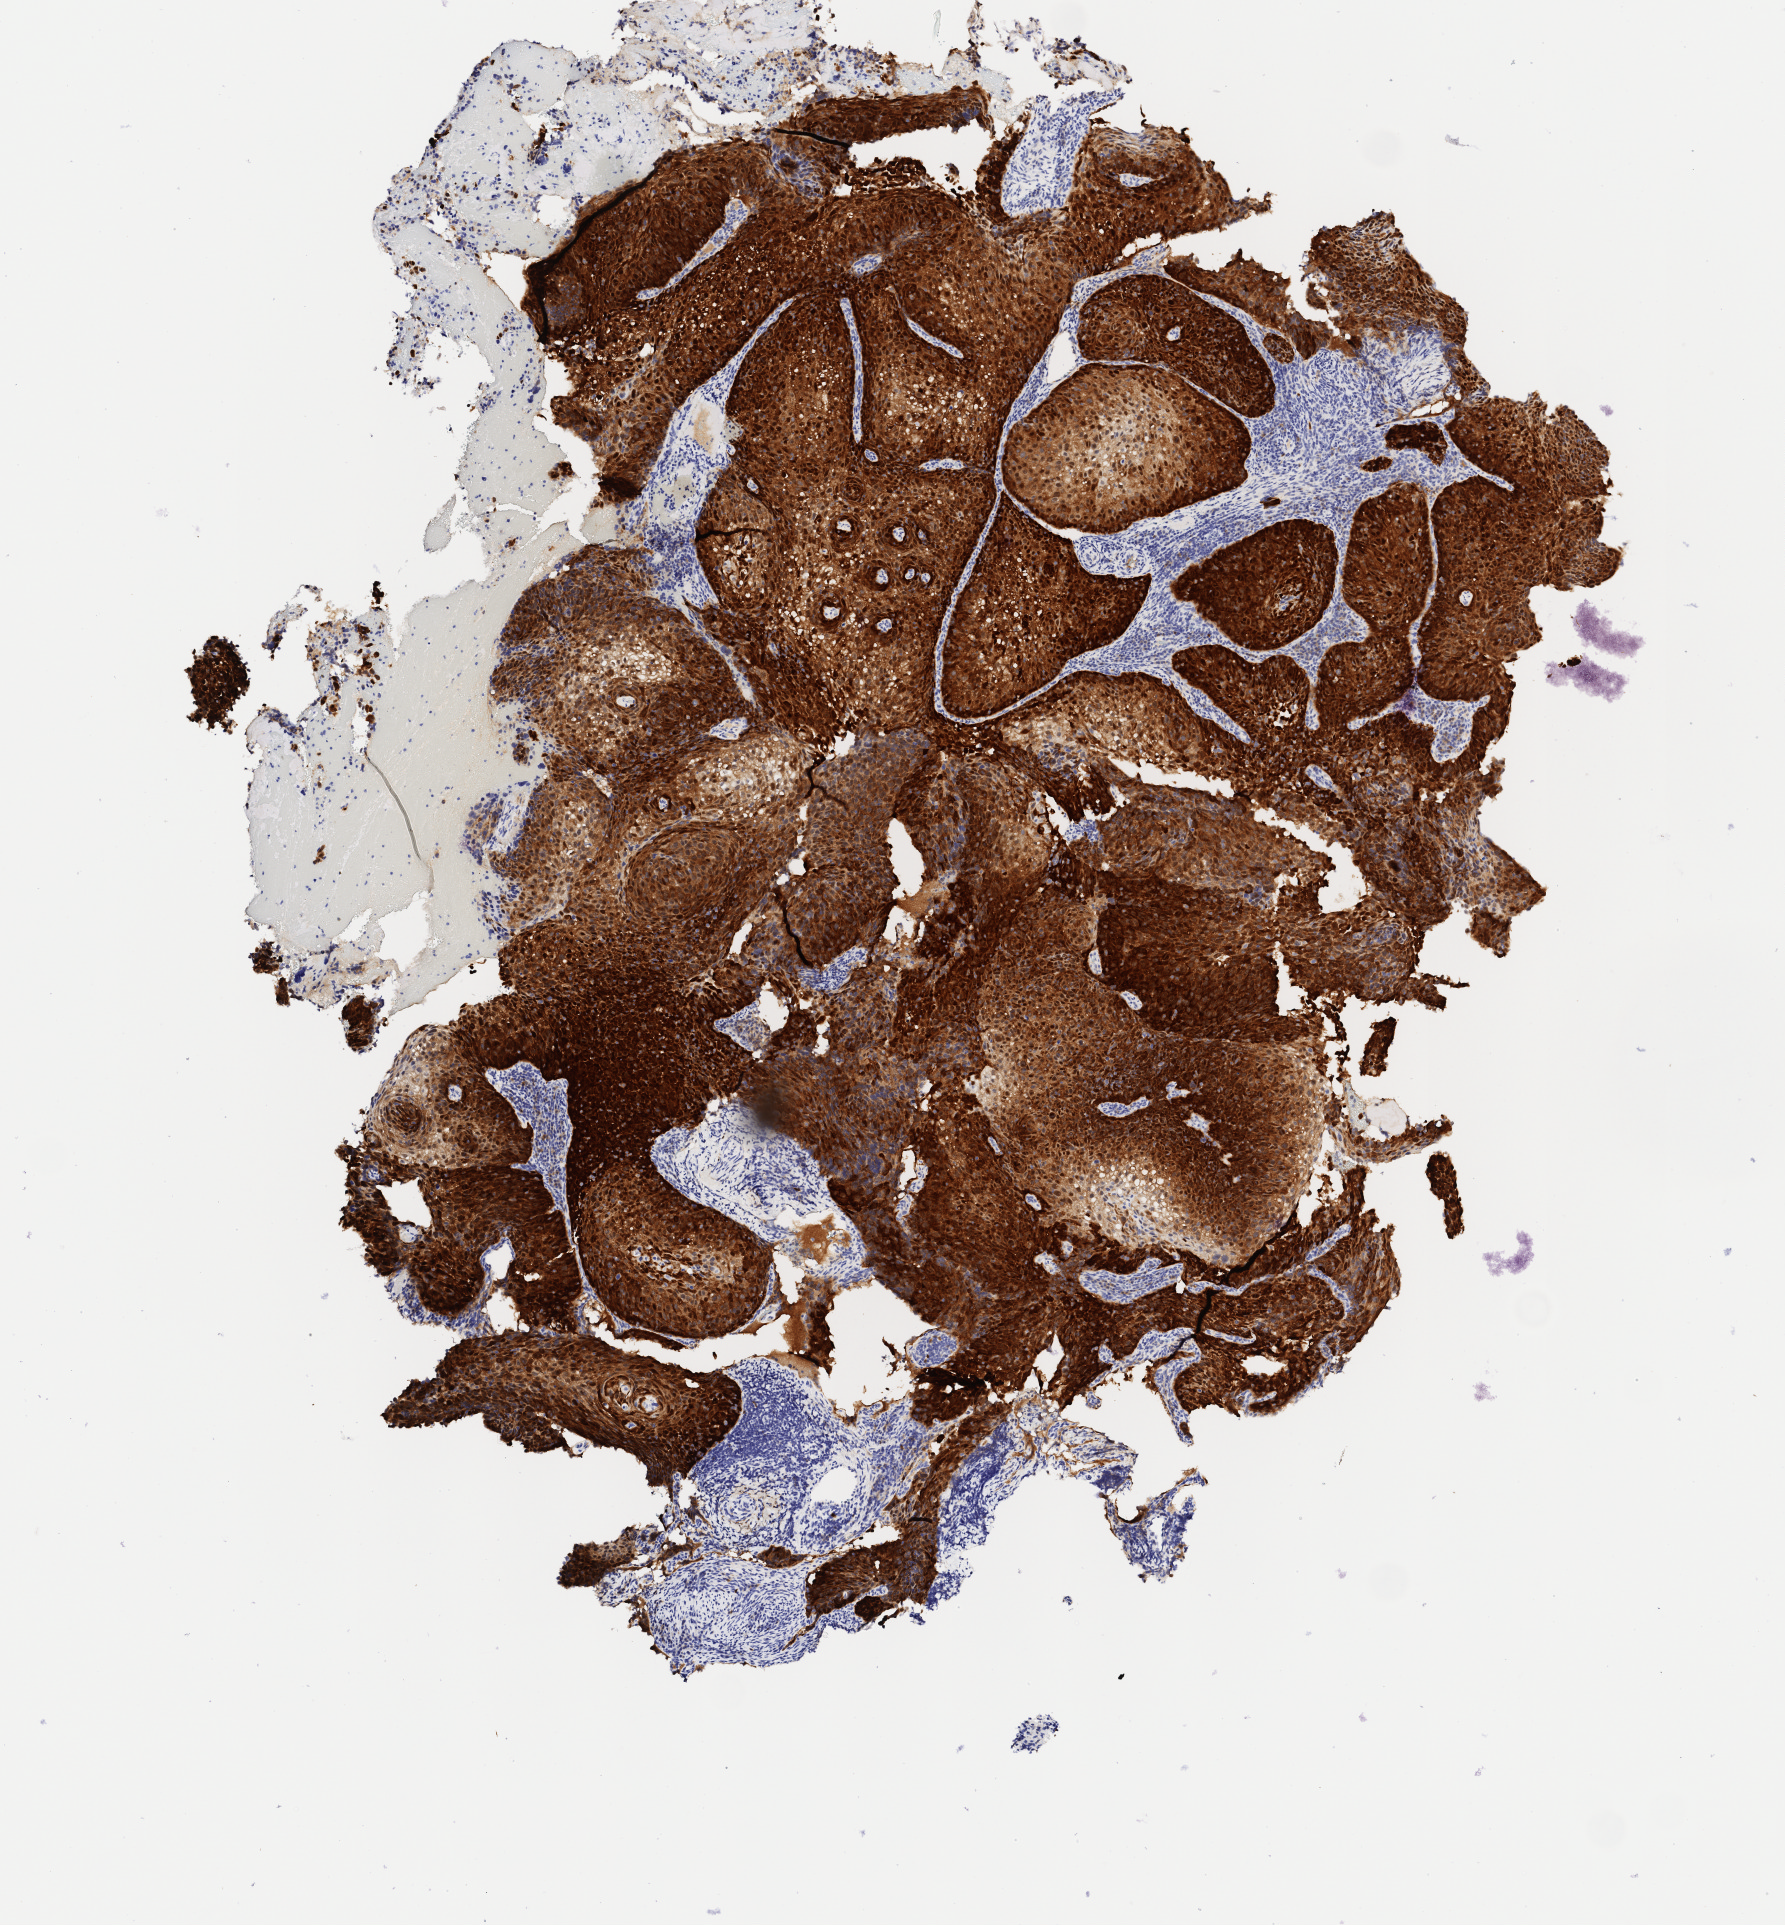
Whole-slide image, immunohistochemical stain for p16 (p16INK4a) — shown as a low-resolution overview of the whole scanned area (about 3.6 x 3.8 mm), tumor tissue, anatomic site: cervix. Patient: female, 30 years old.
Histologic diagnosis: Squamous cell carcinoma, keratinizing, NOS.